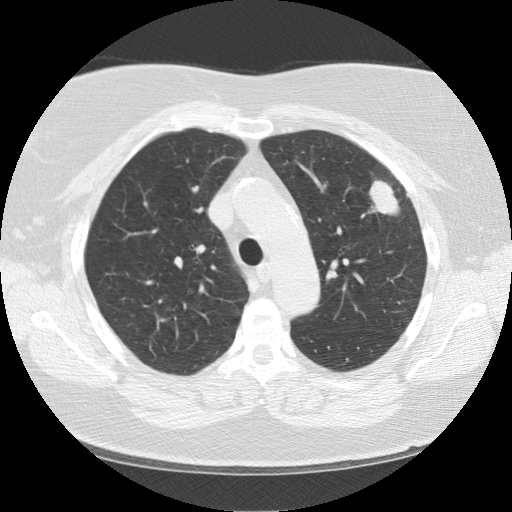
Low-dose screening chest CT, one axial slice; position 95 of 130 along the scan axis; reconstruction kernel STANDARD; 120 kVp; lung window (W 1500 / L -600 HU); 2.5 mm slice thickness; 512 × 512 image matrix, field of view 350 × 350 mm.
Structures marked on this image (expert manual segmentation):
- lesion 1 (tumor, upper lobe of left lung): bounding box <369,181,399,215> (left, top, right, bottom; pixels)